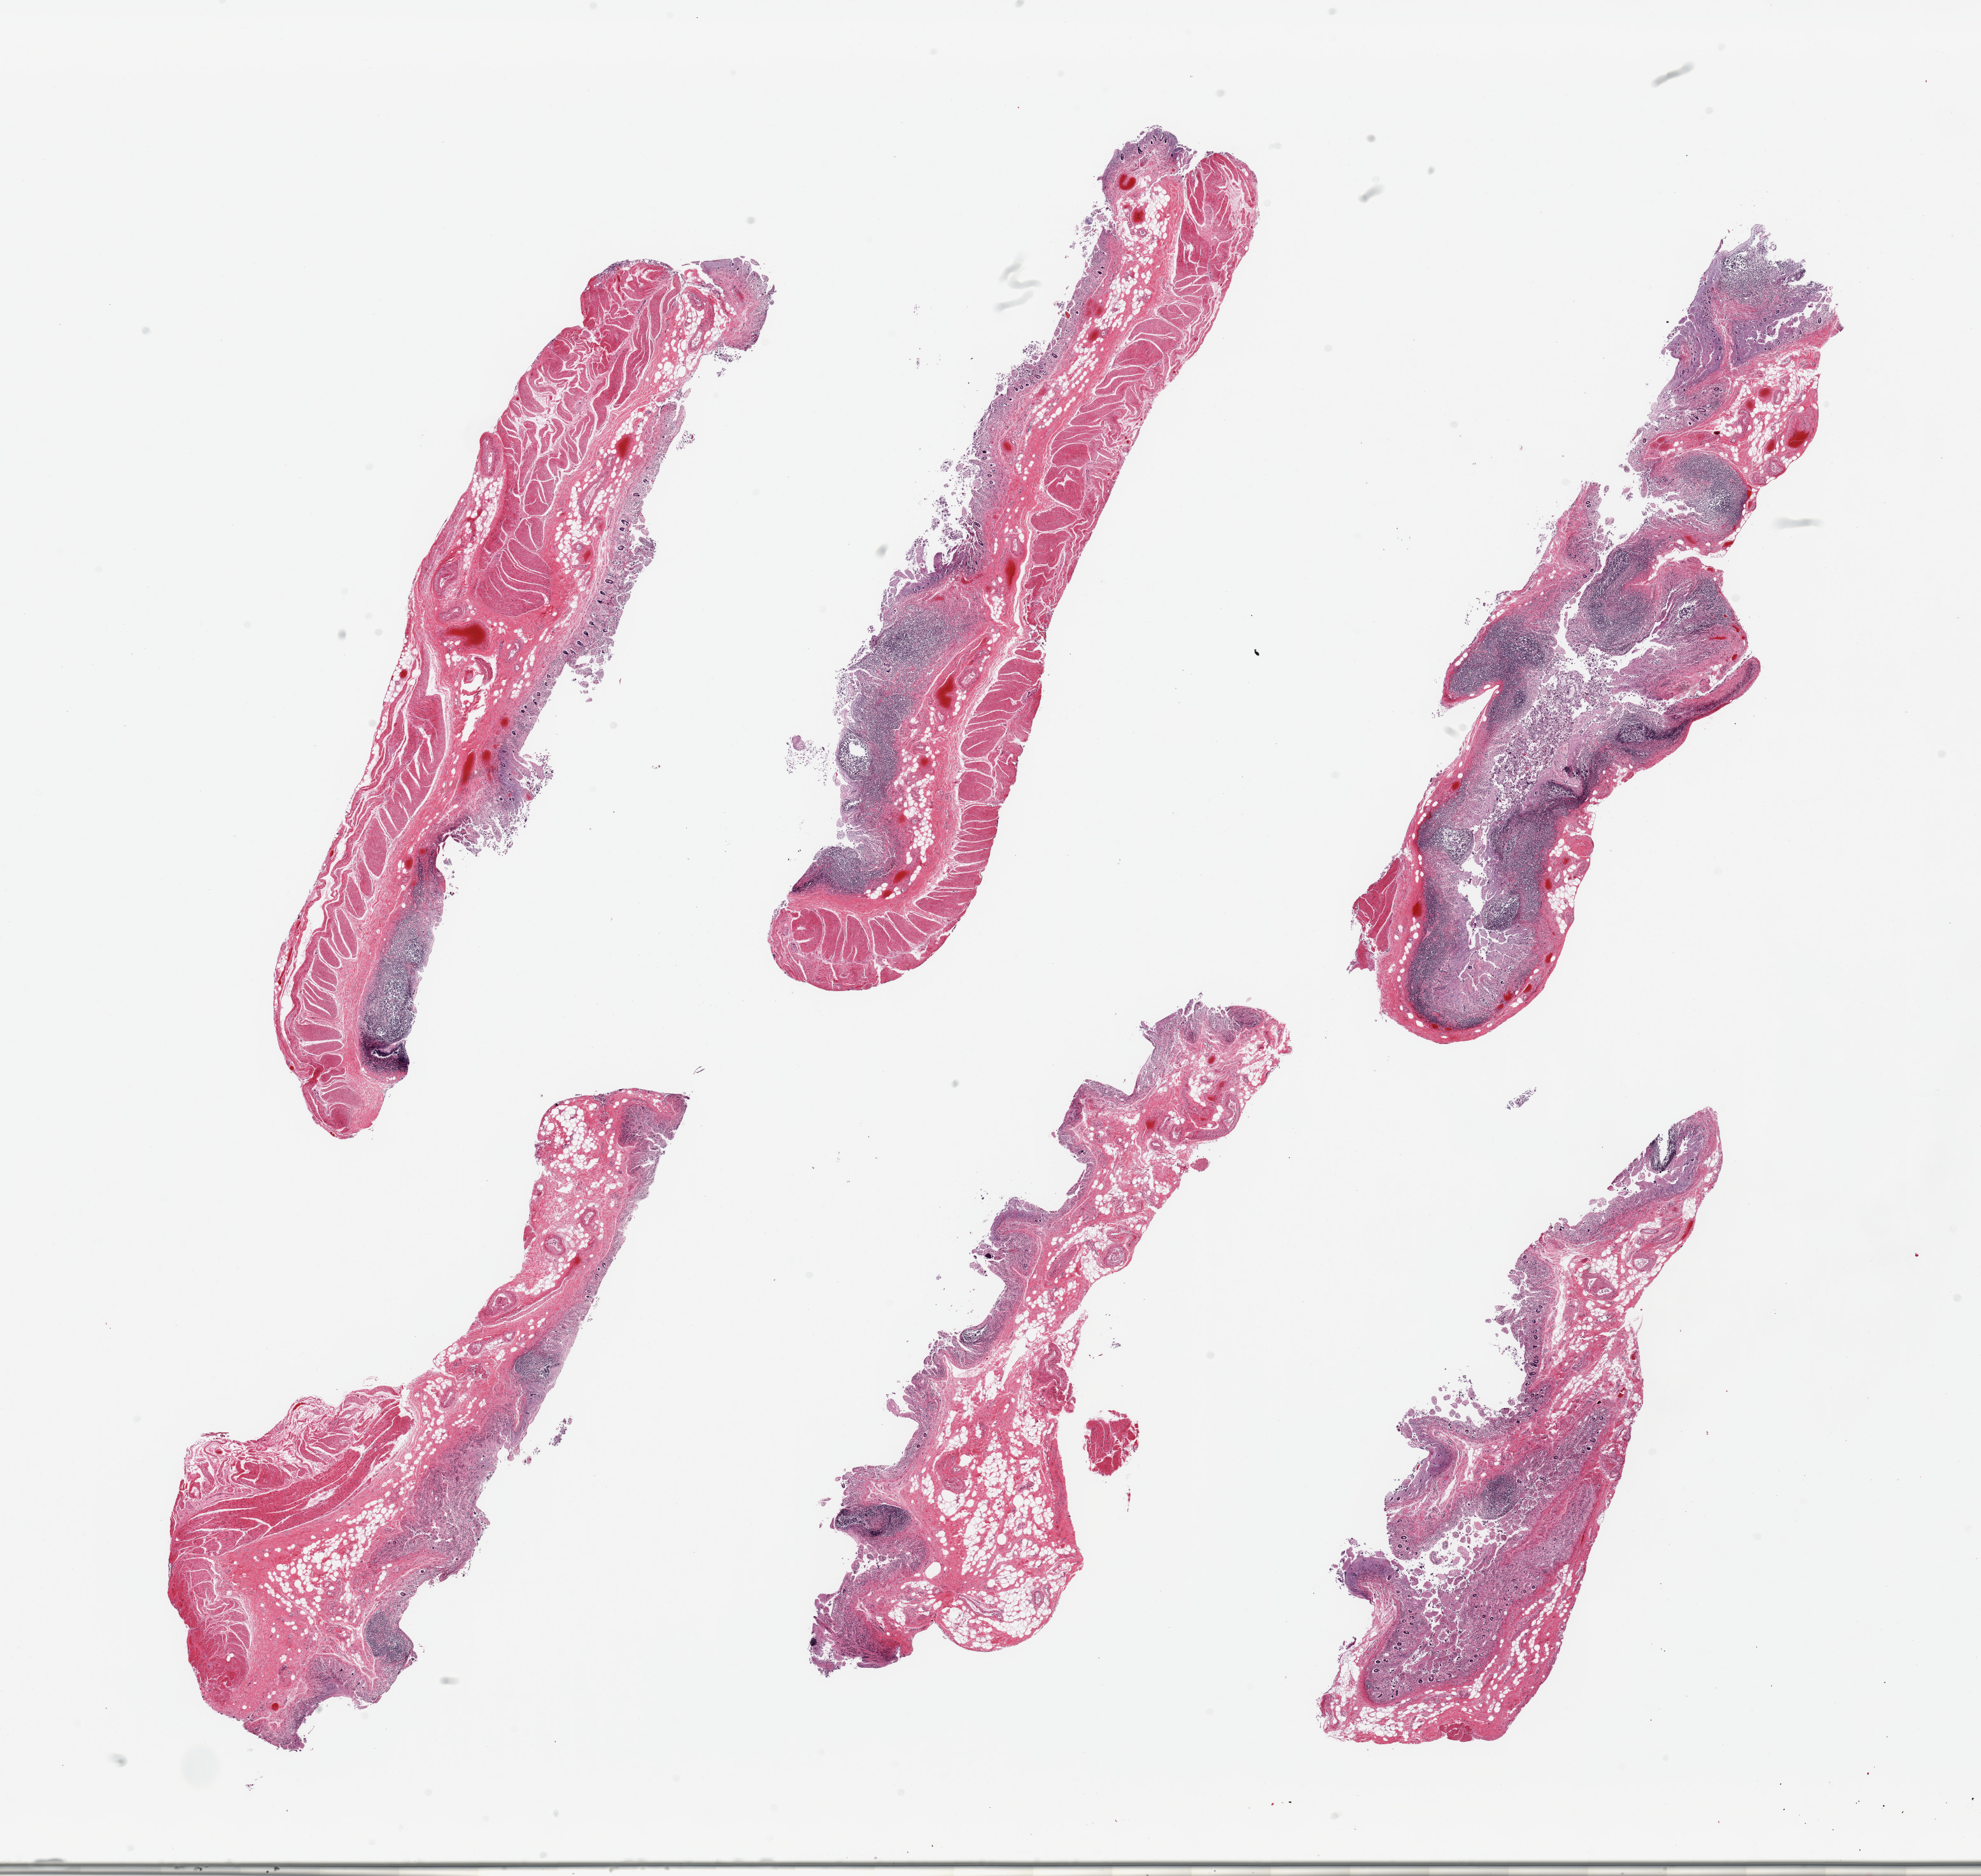
Haematoxylin and eosin whole-slide image — a low-resolution overview of the entire scanned area, about 24.6 x 23.3 mm; PAXgene-fixed paraffin-embedded (PFPE) section; target tissue: ileum; donor tissue sample. Donor sex: male.
* review note (as recorded): 6 pieces; autolyzed mucosa, good lymphoid component (but partially autolyzed), muscularis (not target)